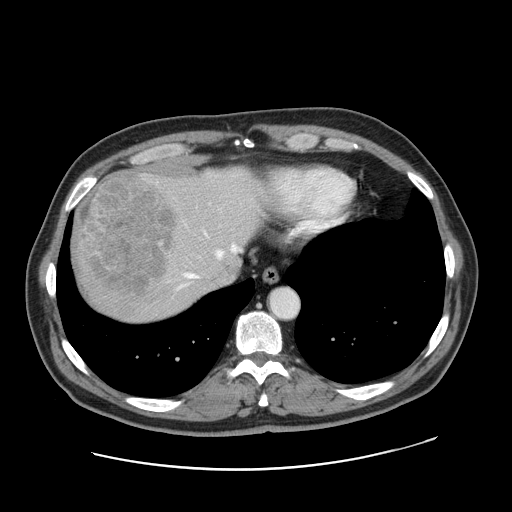
Contrast-enhanced abdominal CT, one axial slice. Position 139 of 178 along the scan axis. 120 kVp. Intravenous contrast given. Soft-tissue window (W 400 / L 40 HU). 2.5 mm slice thickness. 512 × 512 image matrix, field of view 403 × 403 mm. Male patient, age 63 years. From the clinical record (not read from this slice): diagnosis: colorectal cancer liver metastases, imaged before liver resection; multiple liver metastases: yes; largest metastasis: 8 cm; disease in both lobes: yes.
Outlined on this slice (manually delineated by an expert):
- hepatic veins: bounding box [x1, y1, x2, y2] px = [178, 232, 241, 289]
- liver: [71, 165, 270, 323]
- planned liver remnant (the part of the liver to remain after resection): [175, 169, 270, 280]
- portal vein (with intrahepatic branches): [159, 241, 162, 243]
- liver metastasis: [72, 172, 176, 300]